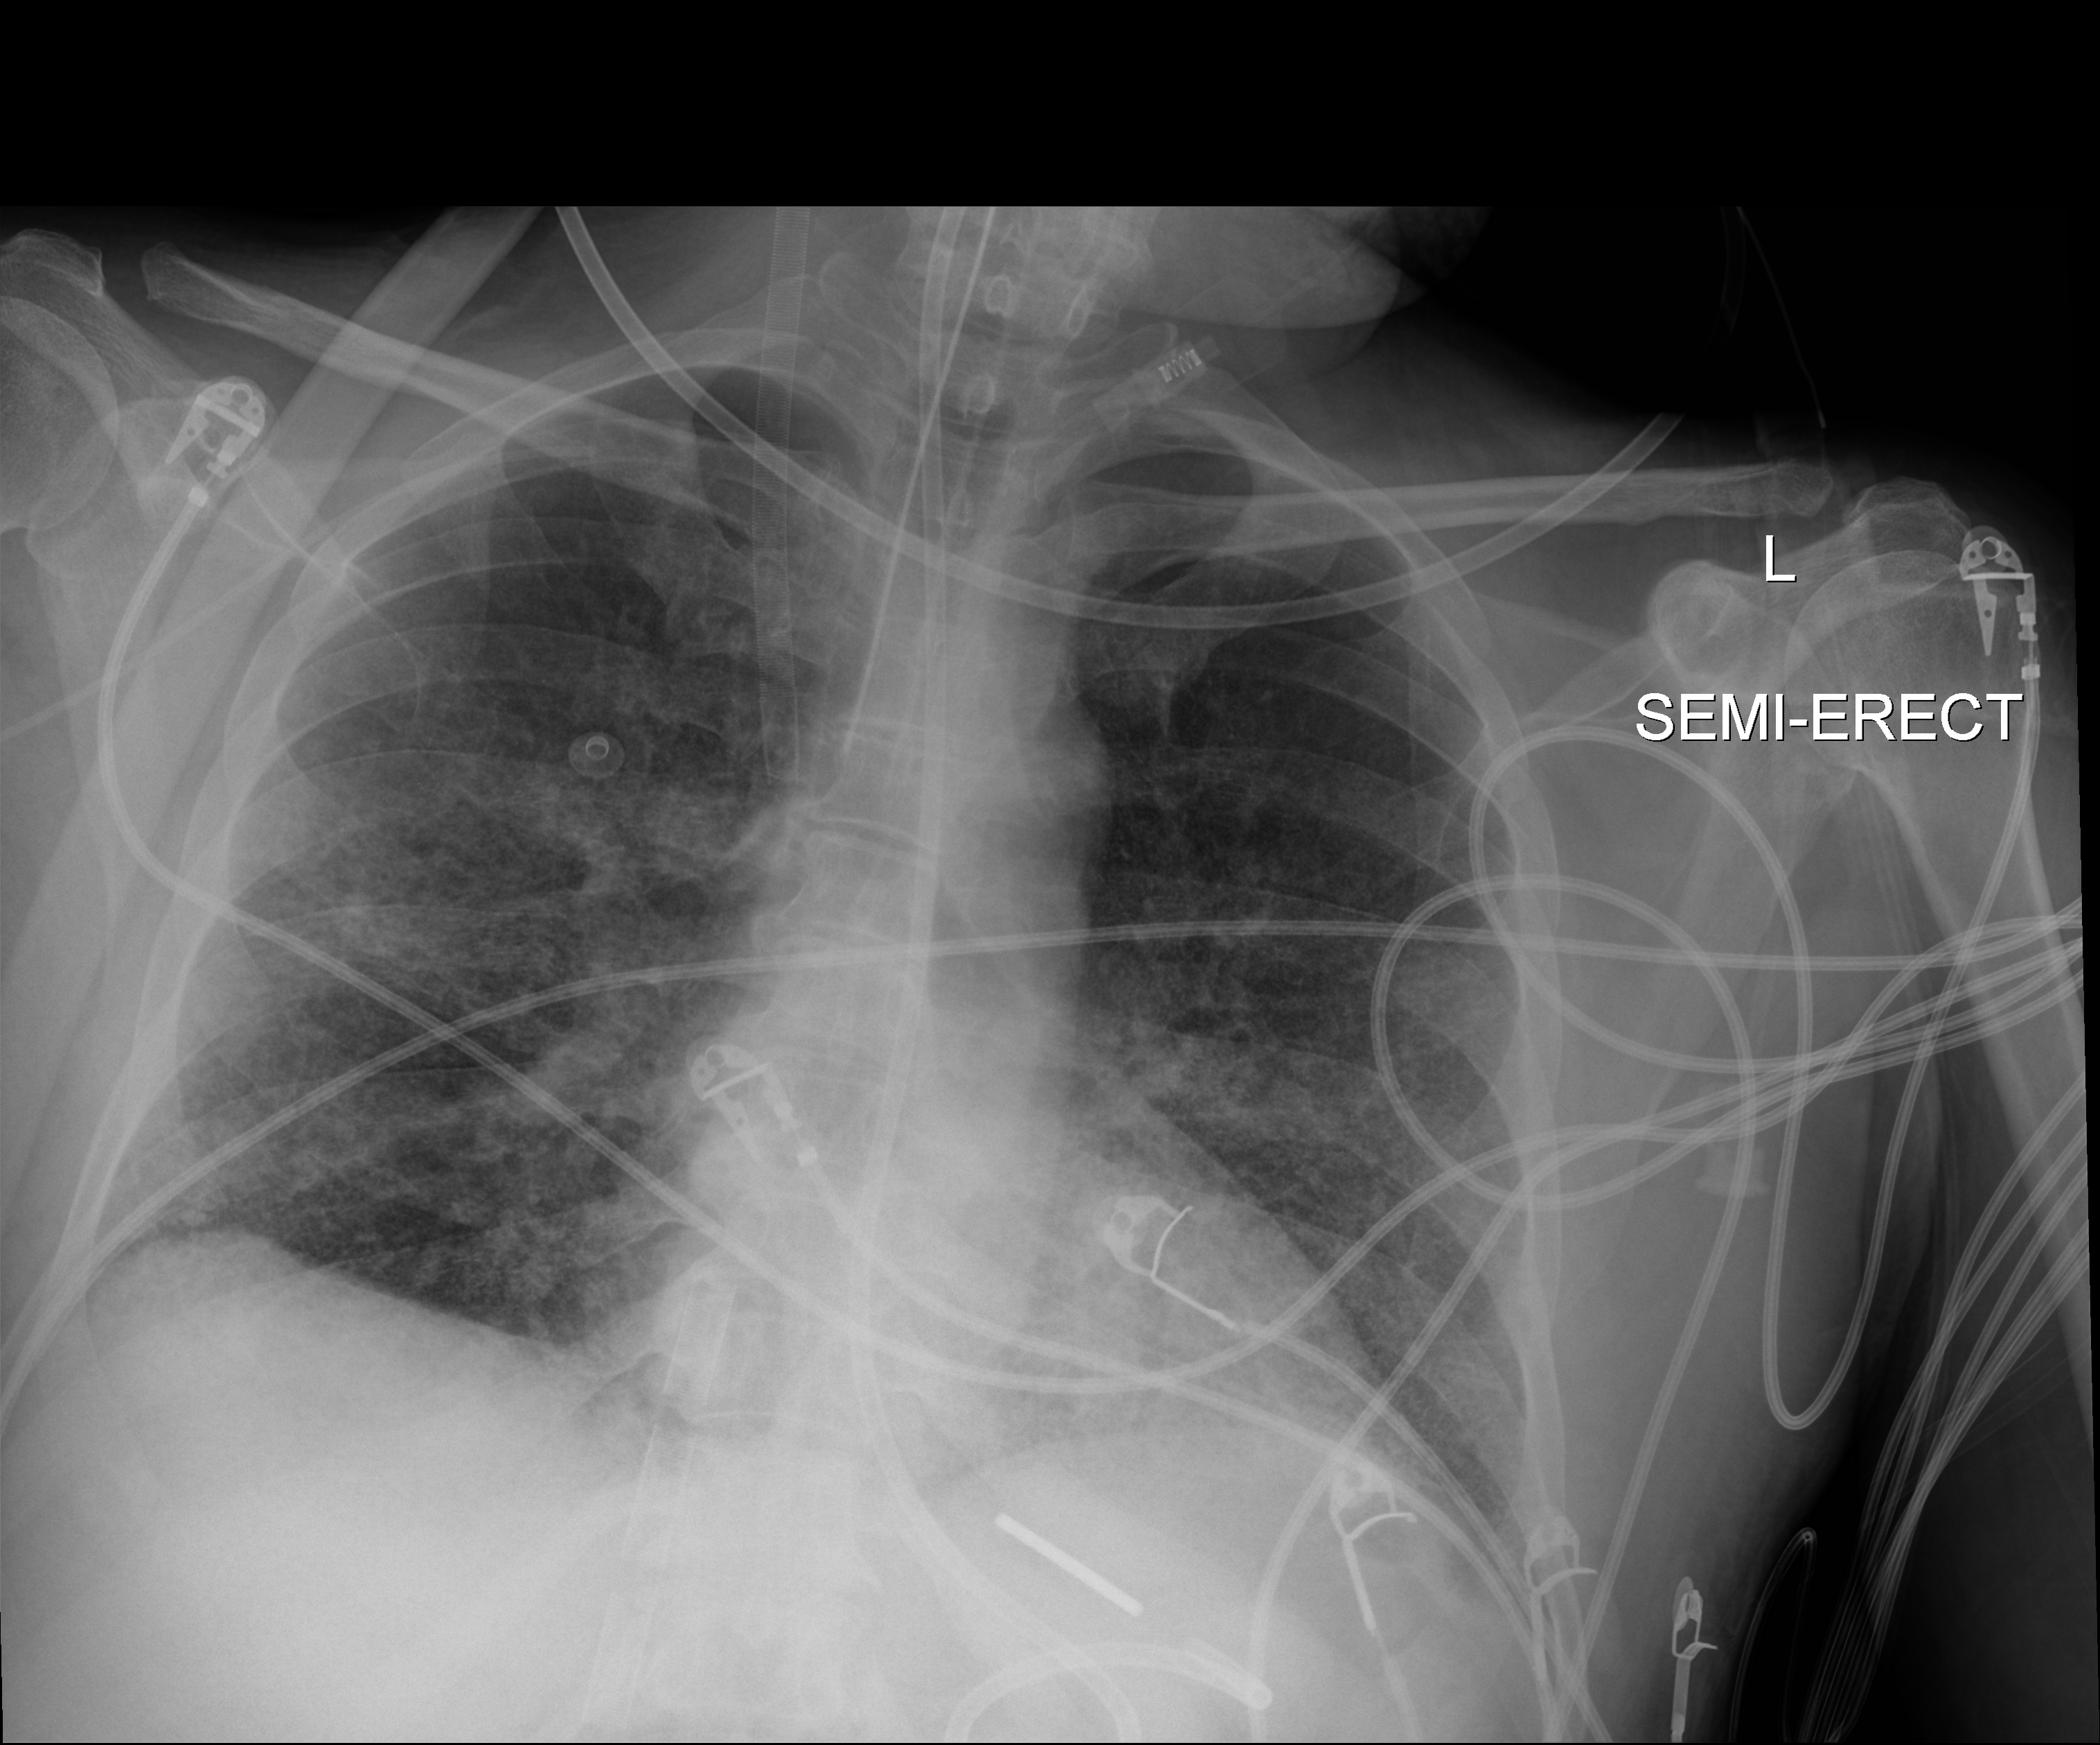
Bedside chest radiograph (digital radiography); anteroposterior (AP) projection. Patient hospitalised with COVID-19; male, aged 18–59 years.
From the hospital-stay record, not from the radiograph (when in the stay this image was taken is not recorded):
- diabetes (admission record): no
- admitted to intensive care during this hospital stay: yes
- COPD (admission record): no